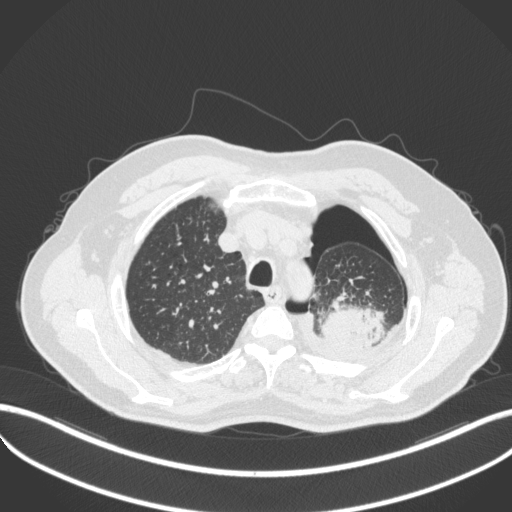
Chest CT, one axial slice; slice 408 of 466 in the series (ordered by position); reconstruction kernel B31f; 120 kVp; lung window (W 1500 / L -600 HU); 512 × 512 image matrix. Patient: male, 76 years. Case-level facts recorded for this patient, not image findings: clinical TNM (as recorded): T3 N0 M1b.
Structures marked on this image (rectangle marked by the reading radiologist):
- lung tumour (recorded histology: adenocarcinoma): bounding box (x1, y1, x2, y2) in pixels: (321, 307, 387, 351)